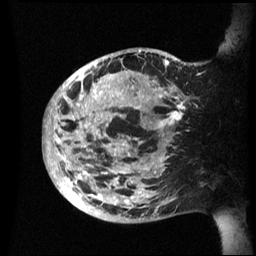
Breast MRI (dynamic contrast-enhanced), one sagittal slice. Slice 18 of 60 in the series (ordered by position). Dynamic contrast-enhanced series, image 2 of 3 at this slice position (ordered by acquisition). 1.5 T. TE 4.2 ms, TR 8.4 ms. 2.4 mm slice thickness. 256 × 256 image matrix, field of view 230 × 230 mm. Patient: female, 48 years.
Structures marked on this image (semi-automatically segmented with operator editing):
- analysis volume of interest (the breast-tissue region the enhancement analysis was run in; not a lesion): bounding box [x1, y1, x2, y2] px = [44, 48, 202, 223]
- tumour enhancement mask (voxels above the 70 % enhancement threshold inside the analysis volume of interest): [44, 50, 183, 208]